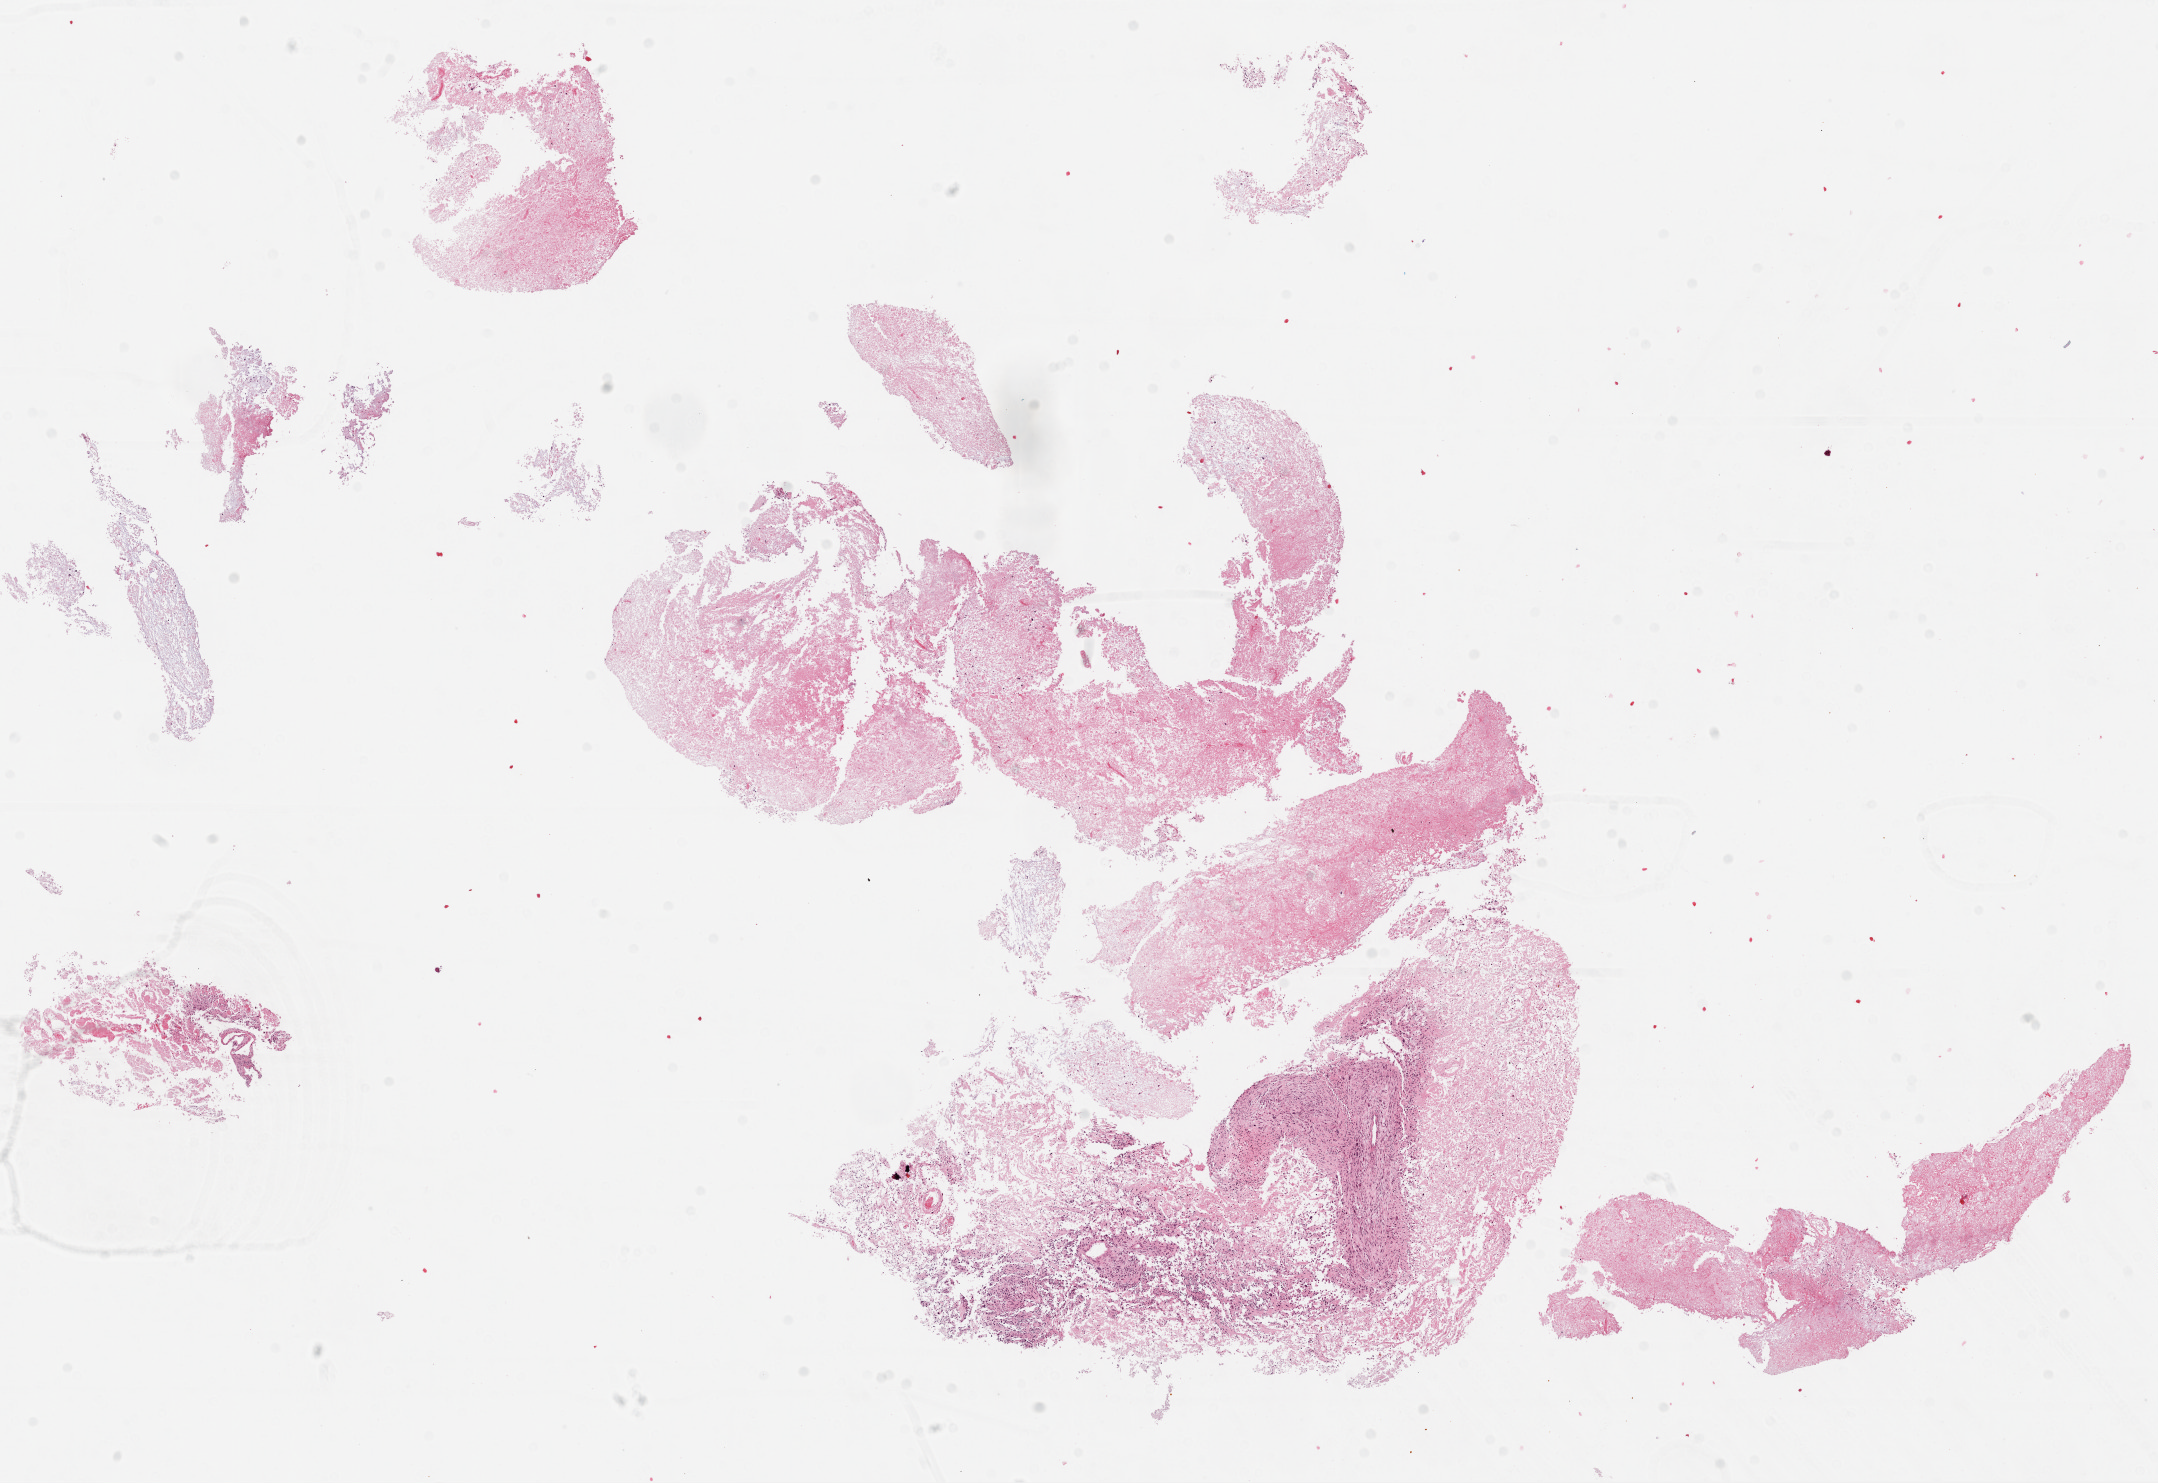
H&E-stained whole-slide image, shown as a low-resolution overview of the whole scanned area (about 17.4 x 12.0 mm, acquisition: 20x scan), formalin-fixed paraffin-embedded (FFPE) diagnostic section, sample: primary tumour, brain. Patient: male, age at initial diagnosis 67 years.
Pathologic diagnosis: Glioblastoma.